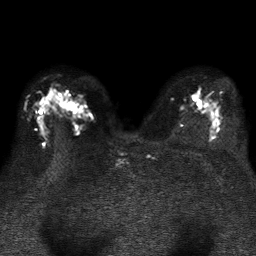
Breast MRI, one axial slice; slice 24 of 37 in the series (ordered by position); diffusion-weighted series; image 2 of 4 stored at this slice position (different b-values; order by instance number); 1.5 T; 5 mm slice thickness; 256 × 256 image matrix. Female patient.
Annotated regions visible in this slice (manually delineated by an expert):
- tumour on diffusion-weighted imaging: bounding box [x1, y1, x2, y2] px = [66, 102, 74, 109]